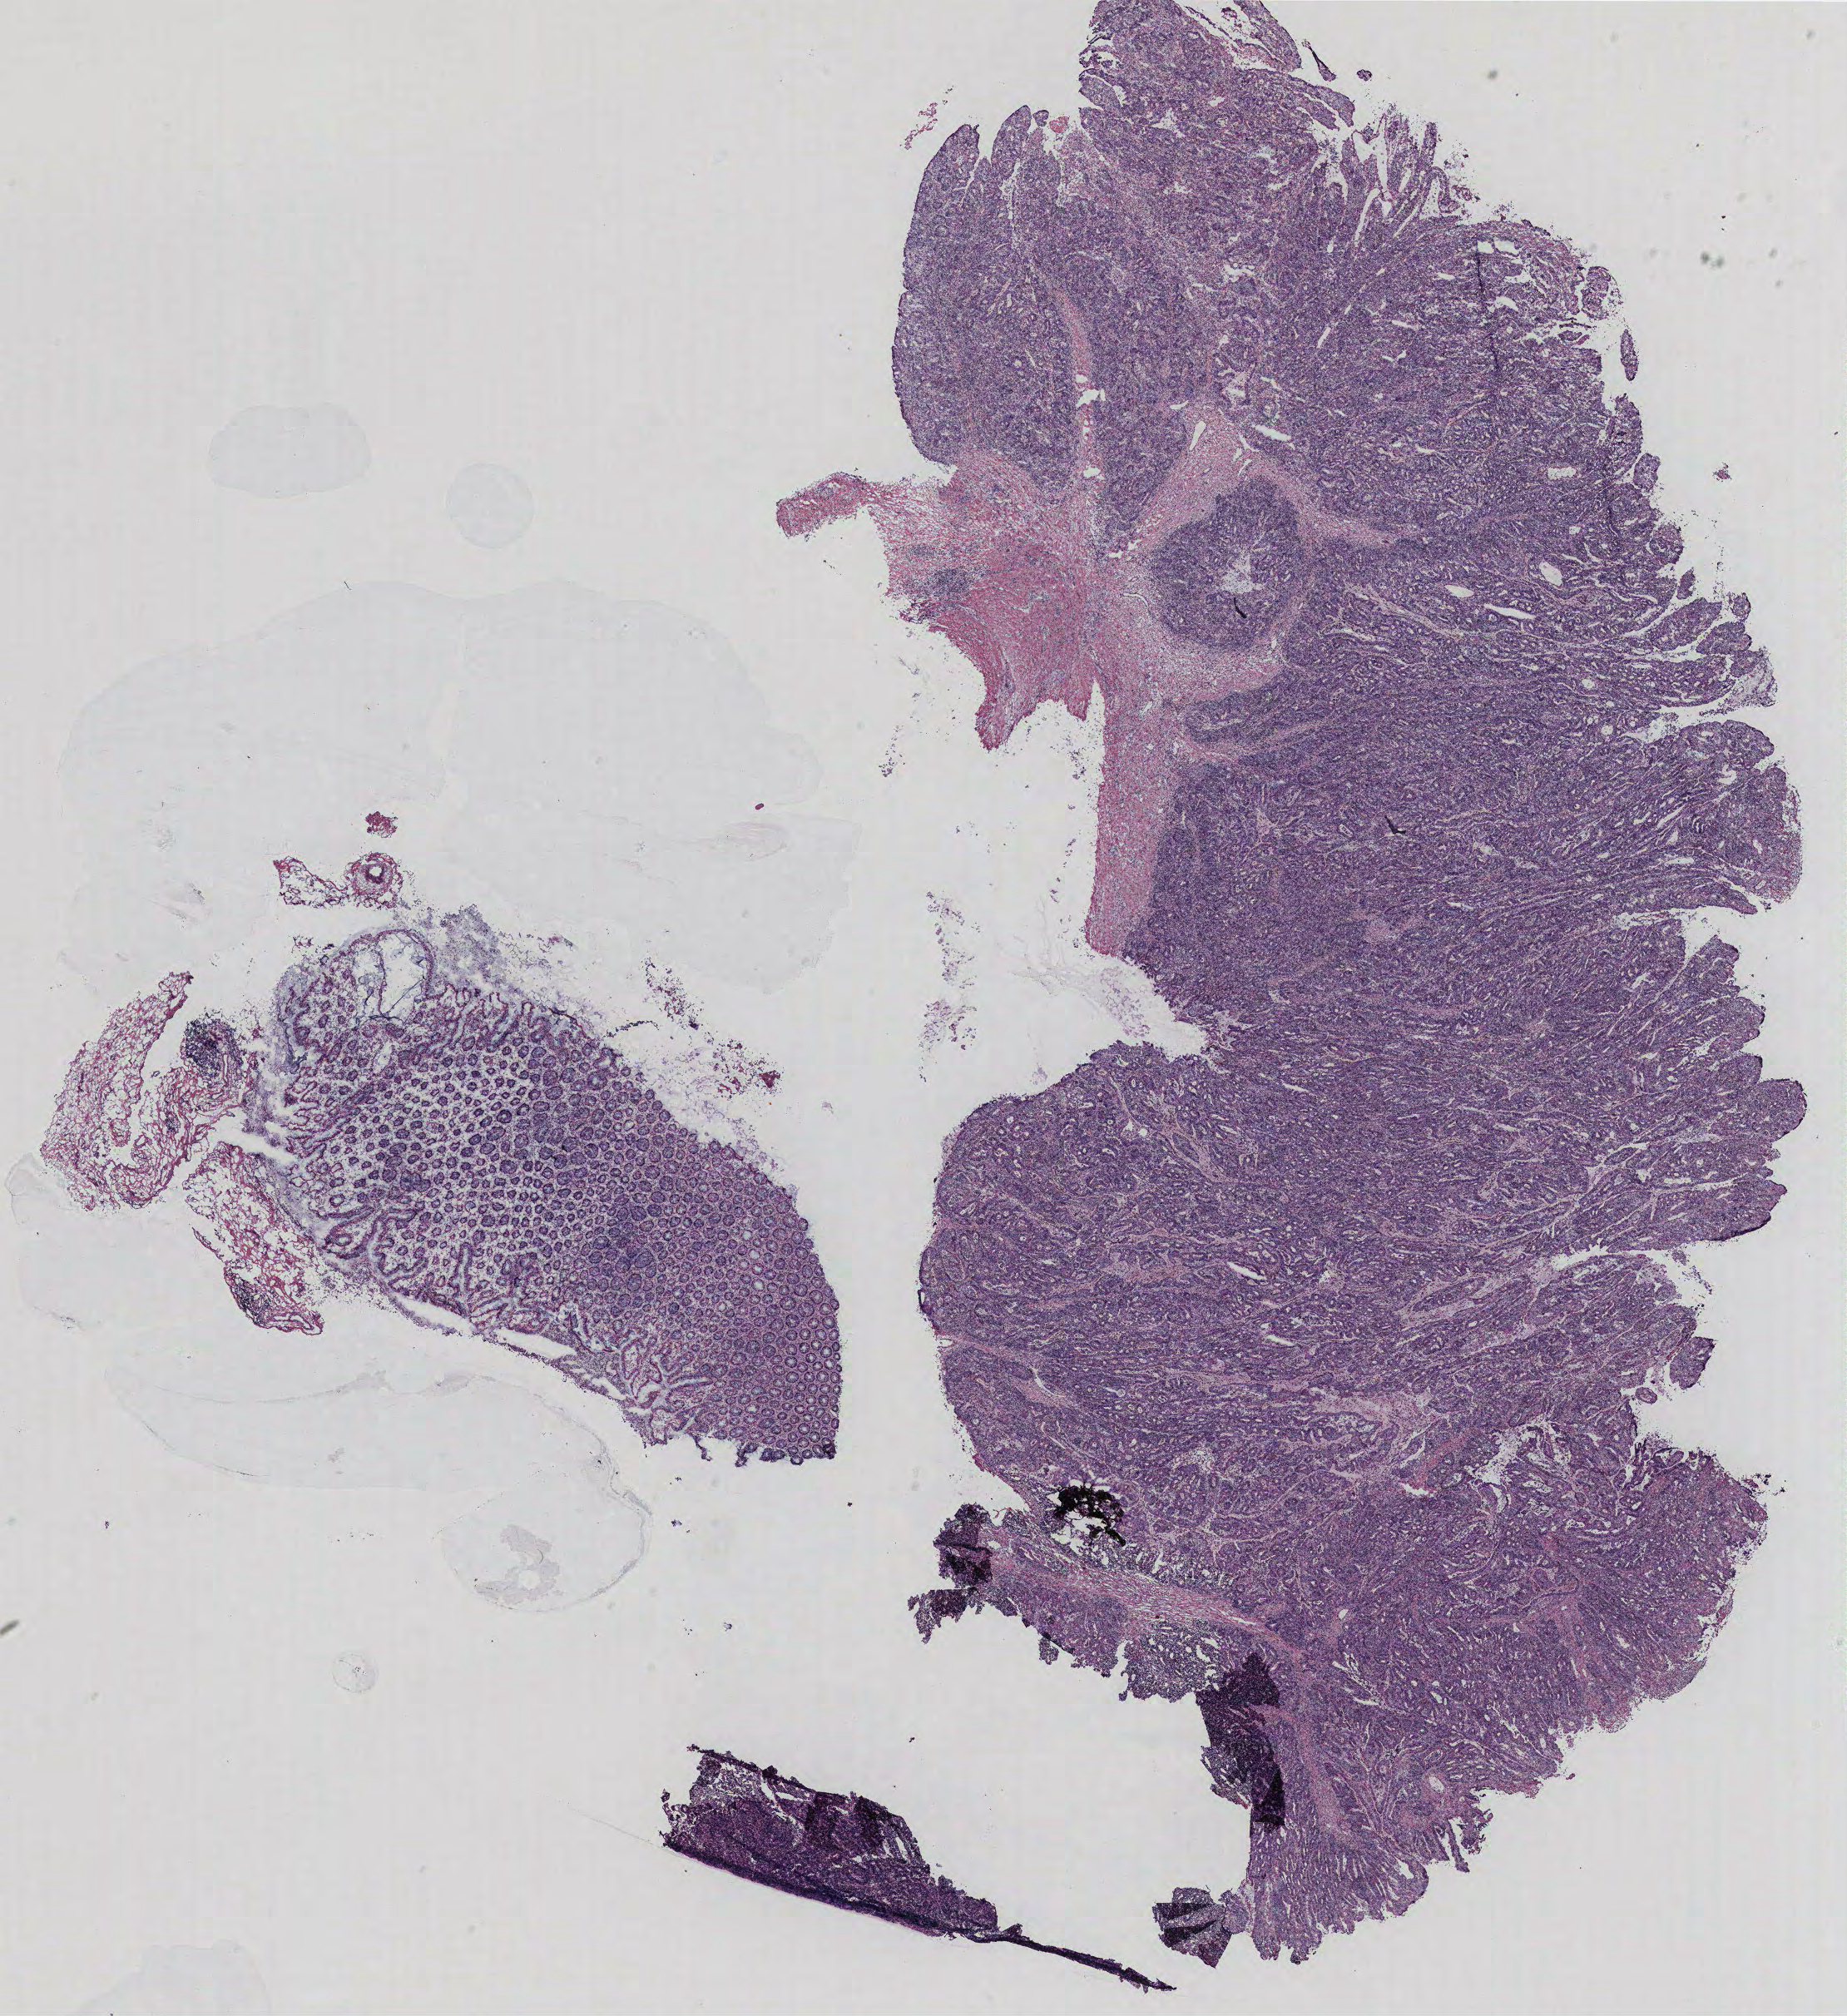
H&E whole-slide image — shown as a low-resolution overview of the whole scanned area (about 17.8 x 19.4 mm, slide scanned at 40x); normal (non-tumour) tissue sample, colon. Female, 53 y/o.
This section: normal (non-tumour) tissue from the same patient. Patient diagnosis: Adenocarcinoma, NOS.